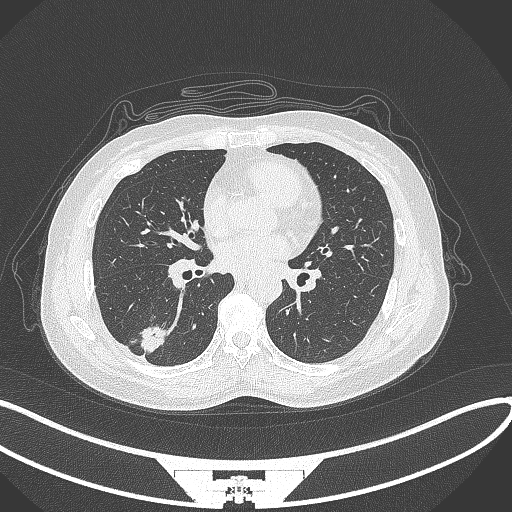
Chest CT, one axial slice. Position 138 of 352 along the scan axis. Lung window (W 1500 / L -600 HU). 1 mm slice thickness. 512 × 512 image matrix. Female patient, age 55 years. From the clinical record (not read from this slice): clinical TNM (as recorded): T1c N1 M0.
Outlined on this slice (rectangle marked by the reading radiologist):
- lung tumour (recorded histology: adenocarcinoma): box from (x=139, y=323) to (x=169, y=356) px